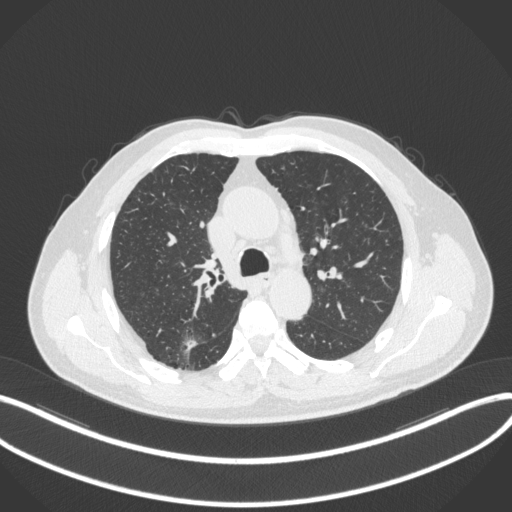
Chest CT, one axial slice. Slice 251 of 366 in the series (ordered by position). Reconstruction kernel B31f. 120 kVp. Lung window (W 1500 / L -600 HU). 1 mm slice thickness. 512 × 512 image matrix, field of view 400 × 400 mm. Male patient, age 69 years. From the clinical record (not read from this slice): clinical TNM (as recorded): T1b N0 M0; histopathological grade: G2-3.
Annotated regions visible in this slice (rectangle marked by the reading radiologist):
- lung tumour (recorded histology: adenocarcinoma): bounding box [x1, y1, x2, y2] px = [178, 336, 200, 355]